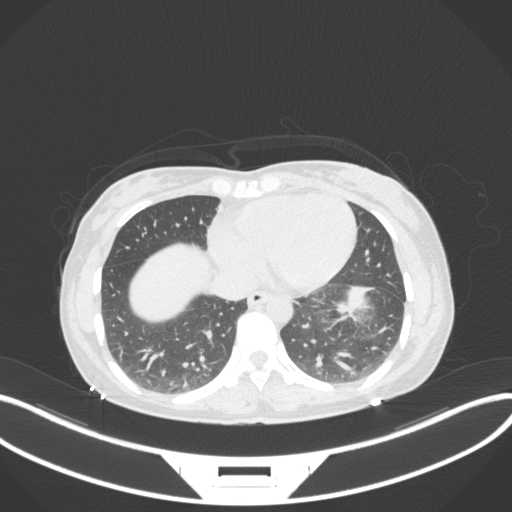
Chest CT, one axial slice. Slice 117 of 361 in the series (ordered by position). Lung window (W 1500 / L -600 HU). 512 × 512 image matrix, field of view 400 × 400 mm. Female patient, age 41 years. From the clinical record (not read from this slice): clinical TNM (as recorded): T2a N3 M1b.
Annotated regions visible in this slice (rectangle marked by the reading radiologist):
- lung tumour (recorded histology: adenocarcinoma): bounding box (x1, y1, x2, y2) in pixels: (329, 280, 377, 319)